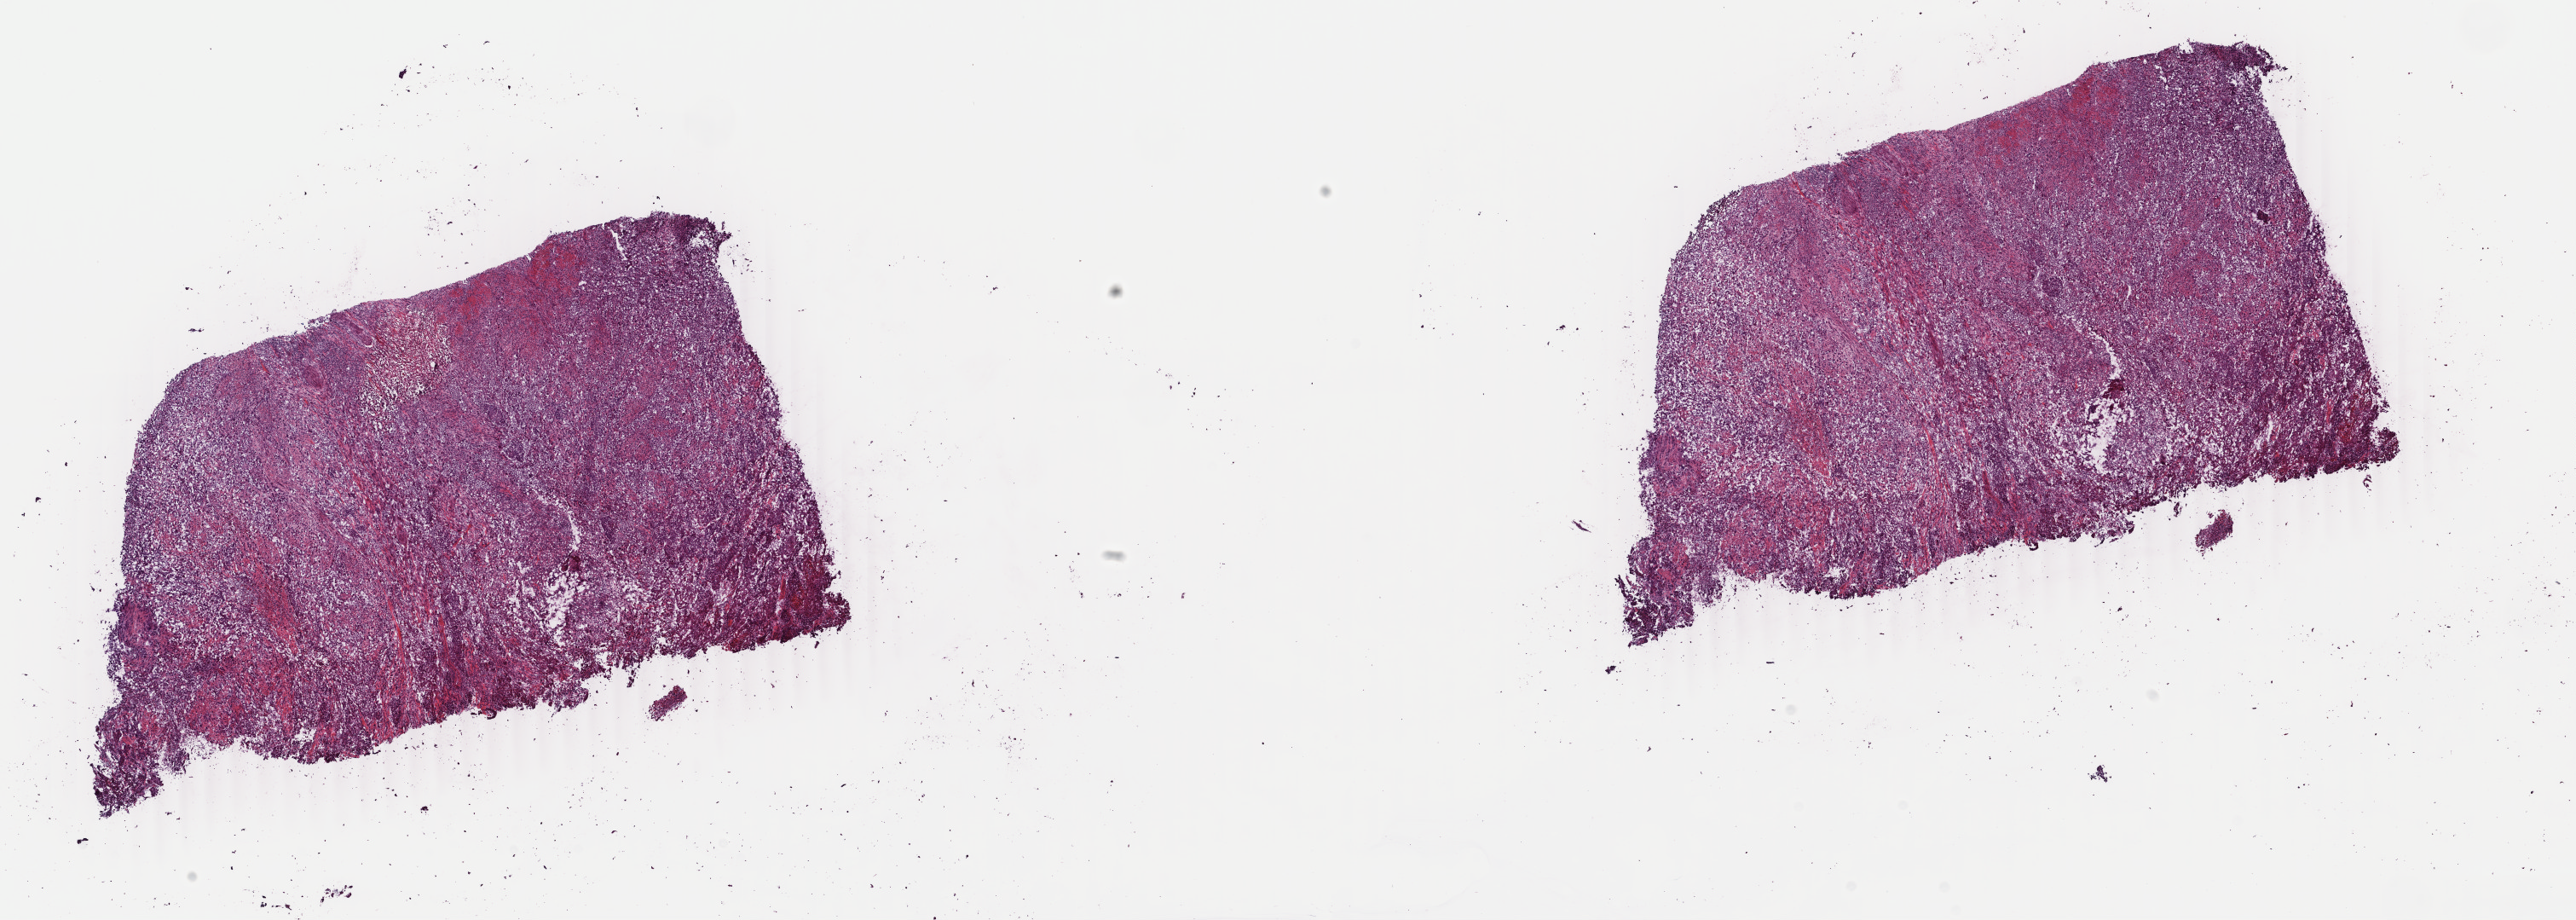
H&E-stained whole-slide image — shown as a low-resolution overview of the whole scanned area (about 24.0 x 8.6 mm), frozen section from the top of the tissue portion, bladder, primary tumour sample. Female, age 63 years at initial diagnosis. Histologic grade: high grade. Slide review estimates, as recorded: tumour cells 75%, tumour nuclei 75%, normal cells 0%, stromal cells 25%, necrosis 0%. Infiltration values recorded for this section: lymphocyte infiltration 5%, monocyte infiltration 0%, neutrophil infiltration 0%.
Diagnosis: Transitional cell carcinoma. AJCC pathologic stage: IV (6th edition).